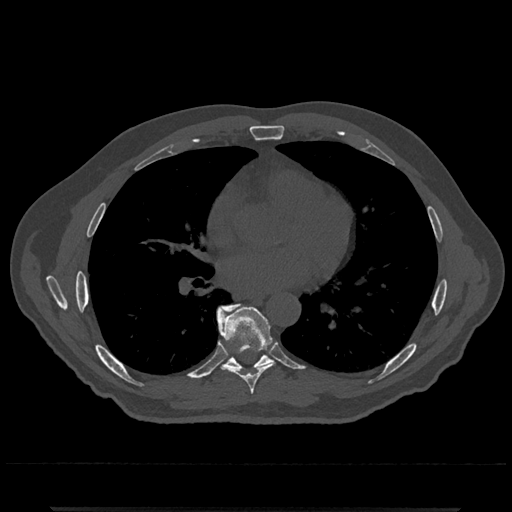
CT including the spine, one axial slice; slice 699 of 797 in the series (ordered by position); 120 kVp; bone window (W 1800 / L 400 HU); 0.5 mm slice thickness; 512 × 512 image matrix. Patient: male, 67 years. Case-level facts recorded for this patient, not image findings: primary cancer: prostate.
Annotated regions visible in this slice (semi-automatic segmentation, software-assisted and operator-edited):
- T7 vertebra: bounding box [x1, y1, x2, y2] px = [219, 308, 274, 394]
- T8 vertebra: [216, 303, 272, 371]